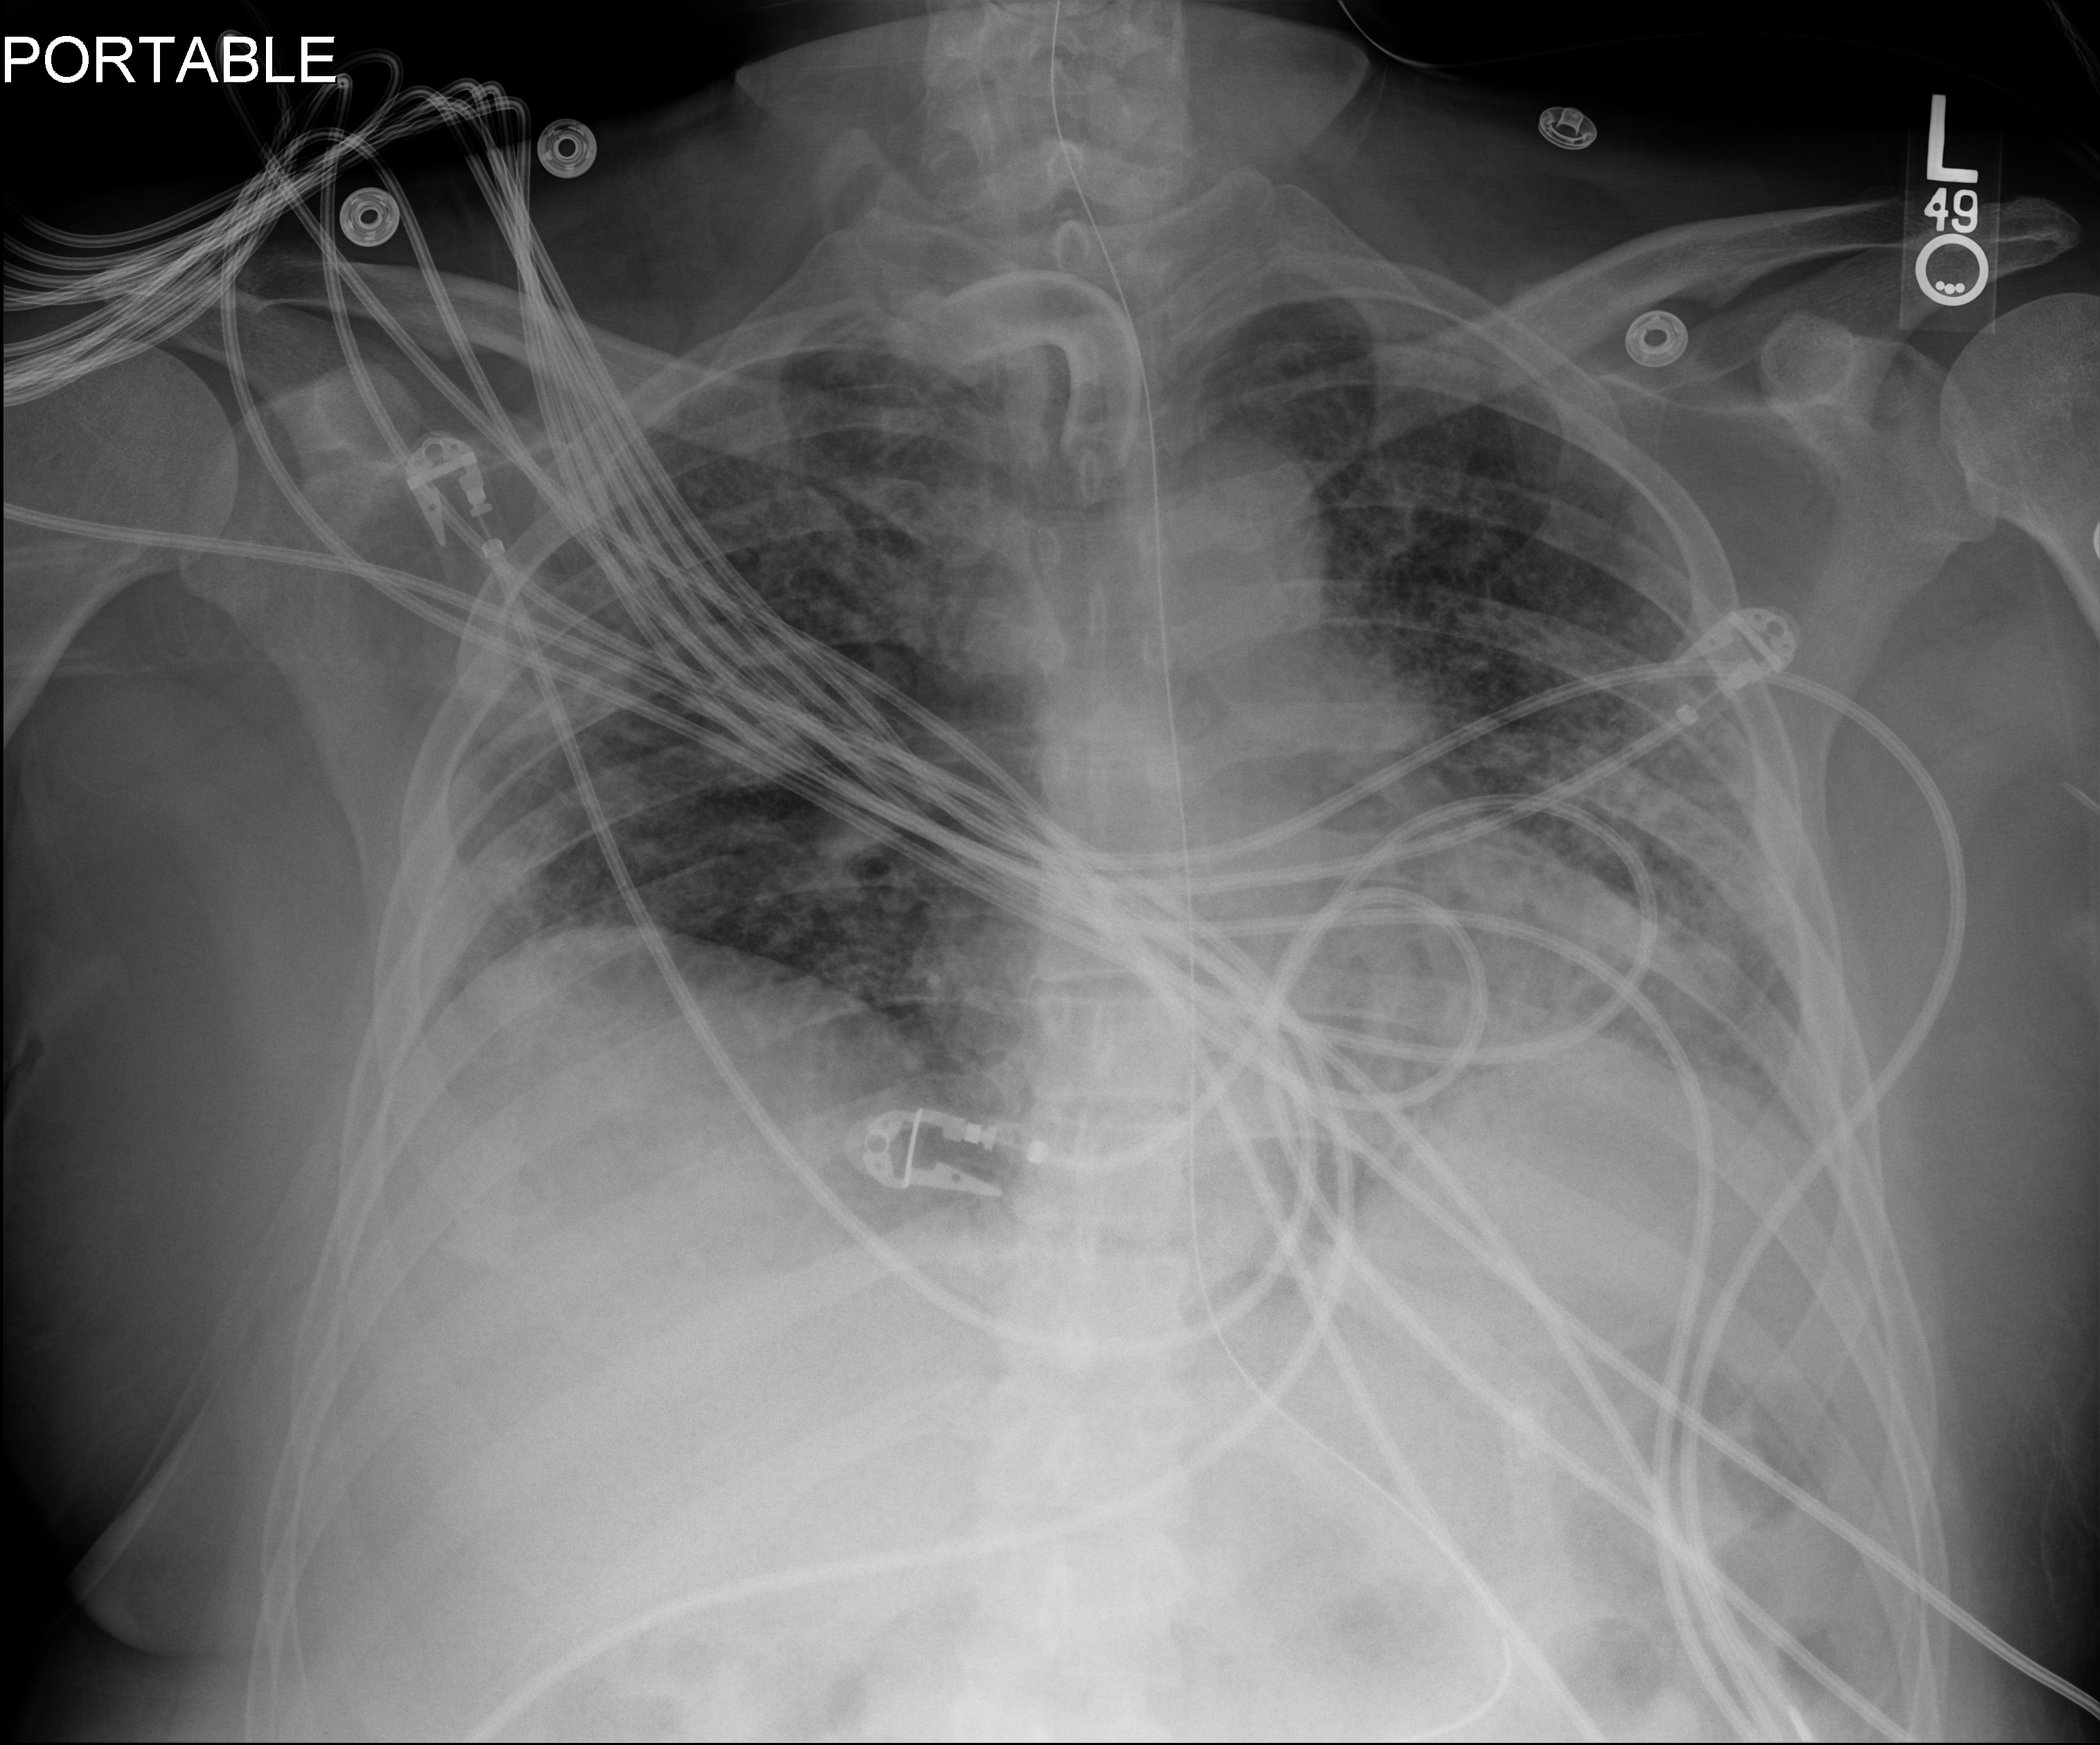
Portable chest radiograph; anteroposterior (AP) projection. Patient hospitalised with COVID-19; male, aged 18–59 years.
Admission-level facts for this patient (not findings on this image; timing relative to this image not recorded):
- other chronic lung disease (admission record): no
- admitted to intensive care during this hospital stay: yes
- length of hospital stay: 96 days